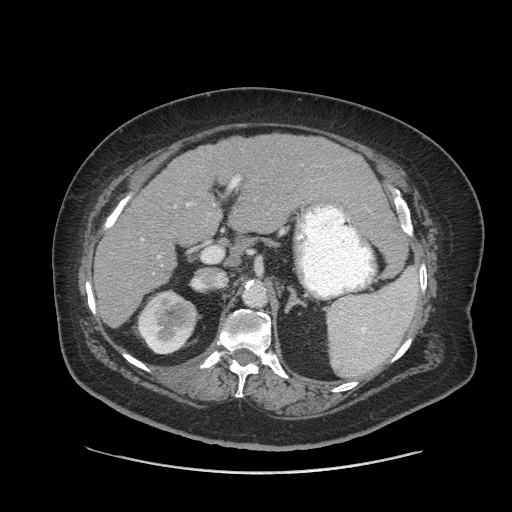
Contrast-enhanced abdominal CT (liver protocol), one axial slice; slice 46 of 91 in the series (ordered by position); 140 kVp; soft-tissue window (W 400 / L 40 HU); 2.5 mm slice thickness; 512 × 512 image matrix. Case-level facts recorded for this patient, not image findings: diagnosis: hepatocellular carcinoma (patient treated with transarterial chemoembolisation; whether this scan precedes or follows treatment is not stated here); TNM stage (as recorded): Stage-I; Child-Pugh class: A; tumour nodularity: uninodular.
Annotated regions visible in this slice (semi-automatically segmented with operator editing):
- liver parenchyma outside the tumour (the mass and vessels are separate outlines, so this box may not span the whole liver): box from (x=94, y=134) to (x=388, y=327) px
- liver vessels: (x=141, y=177)–(x=240, y=258)